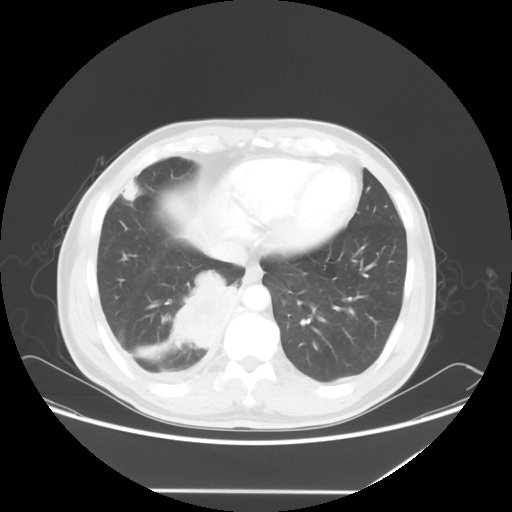
Chest CT, one axial slice. Slice 17 of 60 in the series (ordered by position). Reconstruction kernel STANDARD. 120 kVp. Lung window (W 1500 / L -600 HU). 5 mm slice thickness. 512 × 512 image matrix, field of view 419 × 419 mm. Male patient, age 48 years. Case-level facts recorded for this patient, not image findings: clinical TNM (as recorded): T3 N3 M1a.
Annotated regions visible in this slice (rectangle marked by the reading radiologist):
- lung tumour (recorded histology: squamous cell carcinoma): bounding box <169,267,237,355> (left, top, right, bottom; pixels)